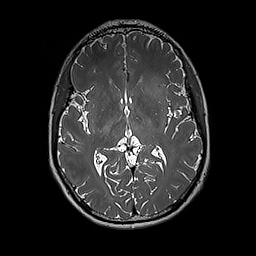
Brain MRI from a brain-tumour surgery series, one axial slice. Position 100 of 192 along the scan axis. 1 mm slice thickness. 256 × 256 image matrix, field of view 250 × 250 mm. Case-level facts recorded for this patient, not image findings: histopathology: Glioblastoma; WHO grade: 4; IDH mutation: no.
Structures marked on this image (manually delineated by an expert):
- tumour: box from (x=140, y=76) to (x=171, y=113) px